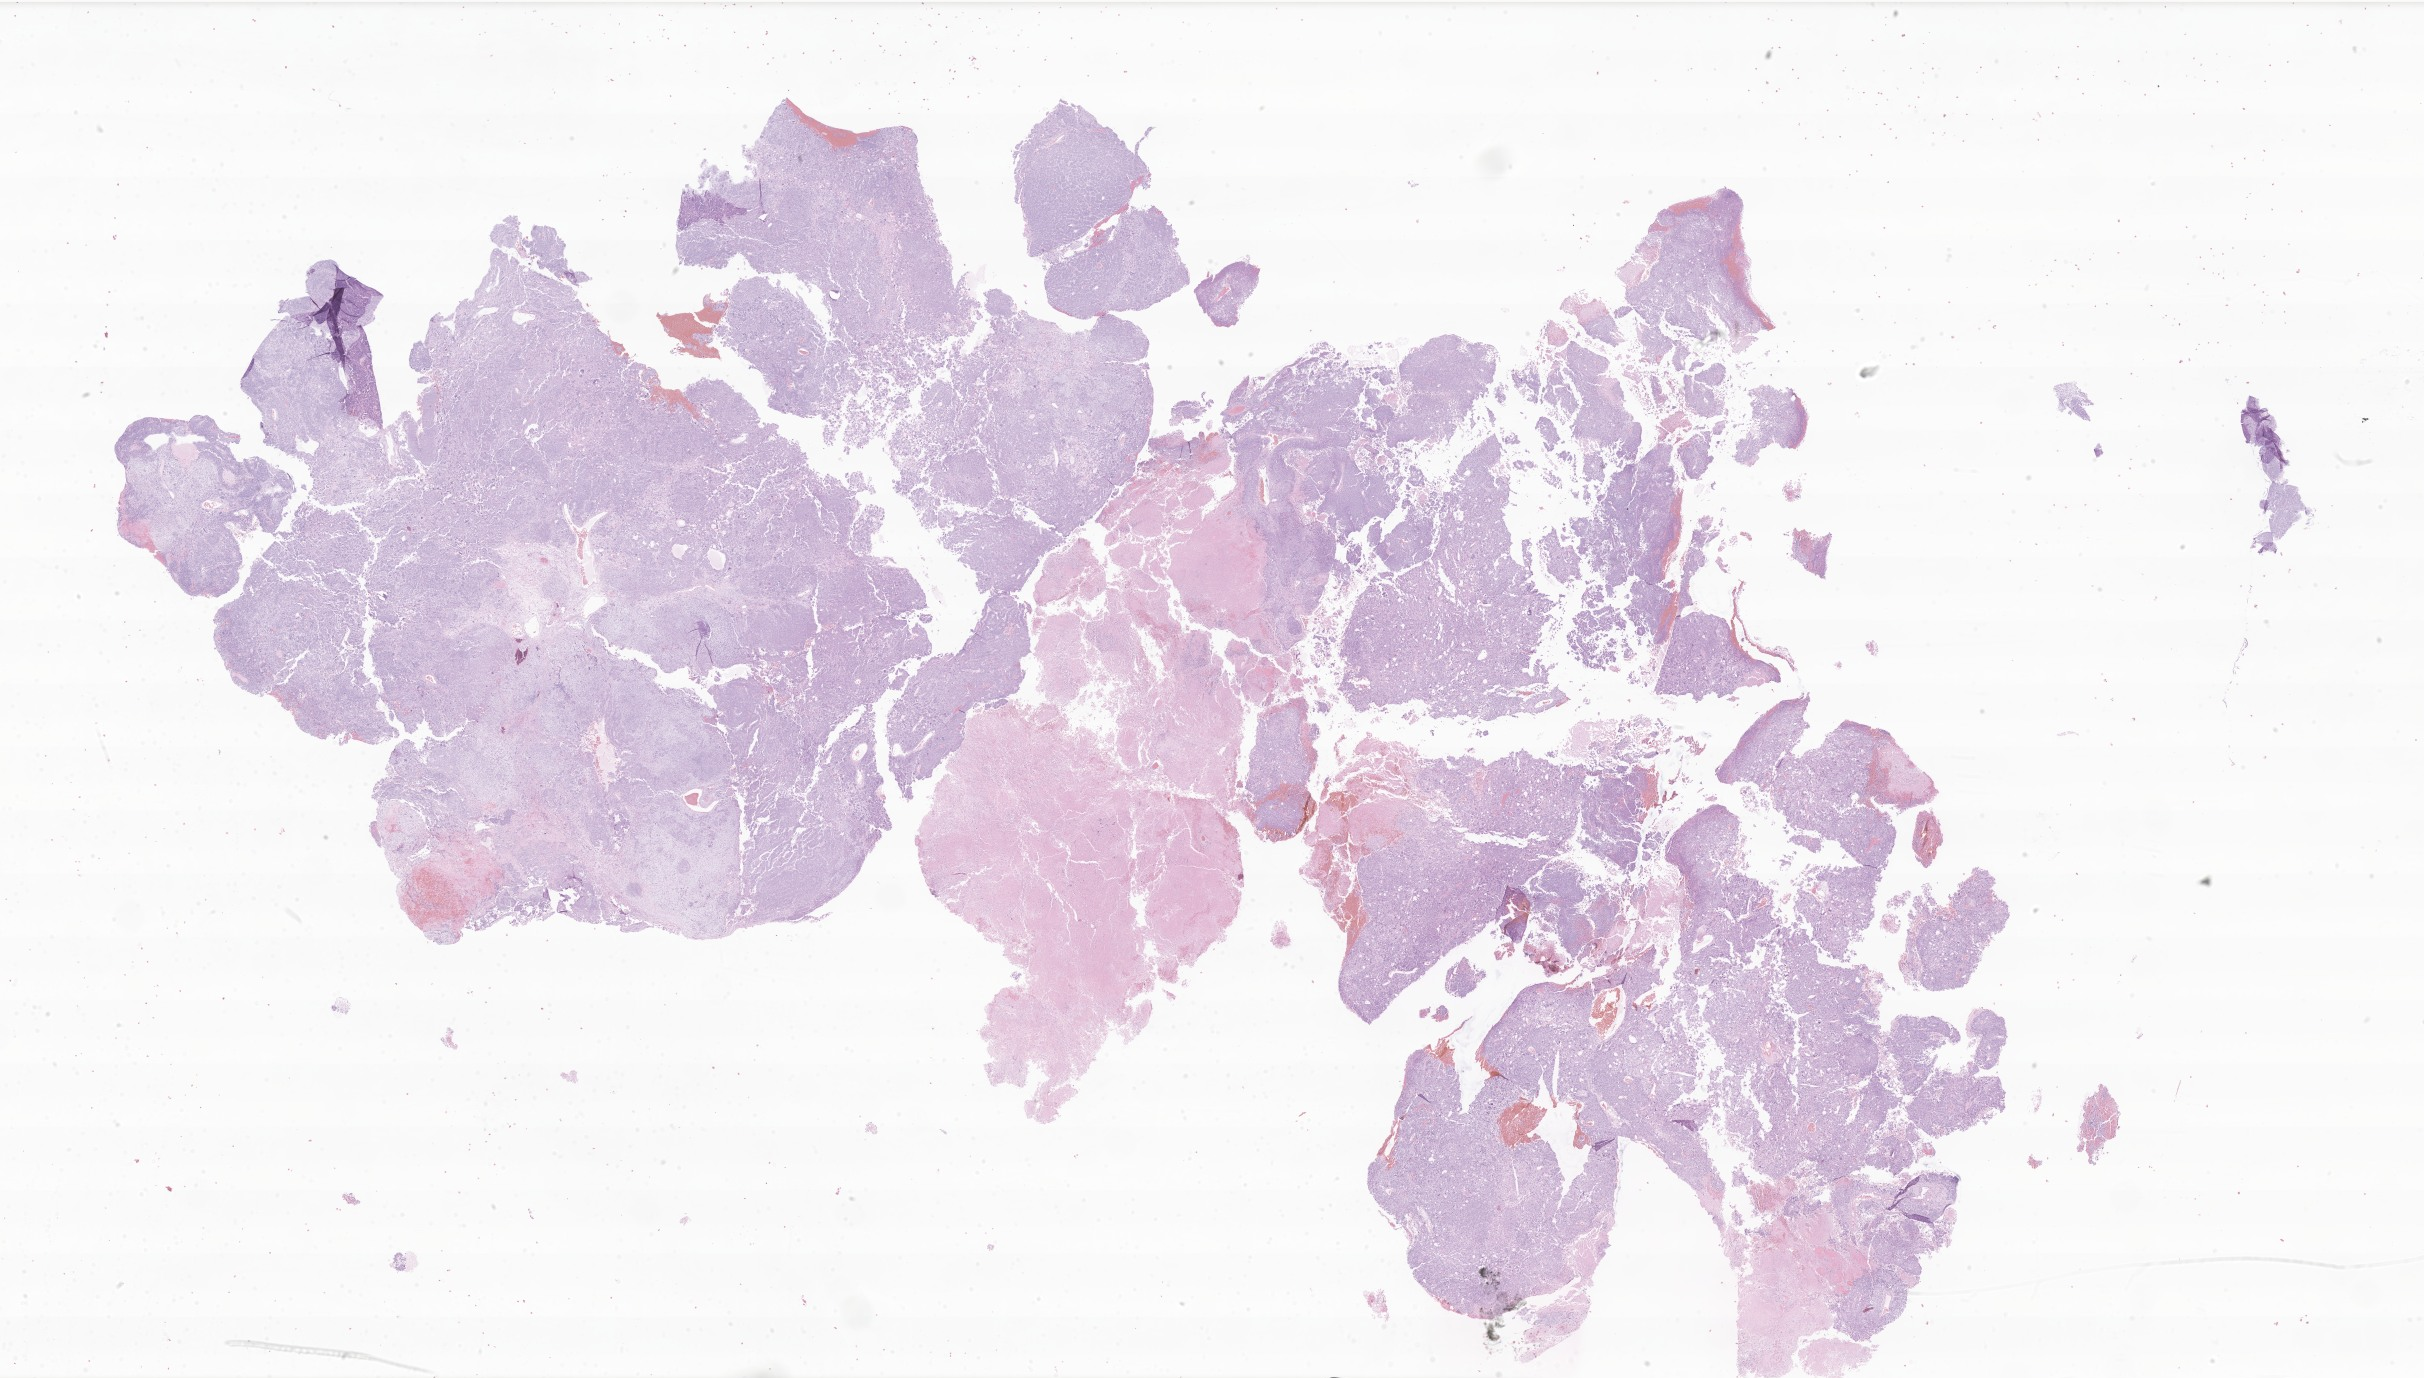
Hematoxylin and eosin (H&E) whole-slide image of tumor tissue from the temporal lobe, shown as a low-resolution overview of the whole scanned area (about 40.9 x 23.2 mm); FFPE section. Male patient, age 93 months (7 years 9 months).
• diagnosis (ICD-O-3 morphology term): CNS embryonal tumor, NOS